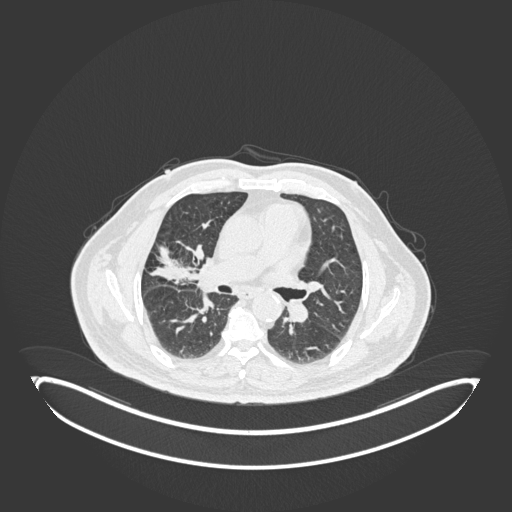
Chest CT, one axial slice. Position 90 of 247 along the scan axis. Reconstruction kernel B30f. Lung window (W 1500 / L -600 HU). 1 mm slice thickness. 512 × 512 image matrix, field of view 500 × 500 mm. Male patient, age 72 years. Case-level facts recorded for this patient, not image findings: clinical TNM (as recorded): T1c N0 M0.
Annotated regions visible in this slice (bounding box drawn by a radiologist):
- lung tumour (recorded histology: squamous cell carcinoma): bounding box [x1, y1, x2, y2] px = [178, 249, 212, 296]